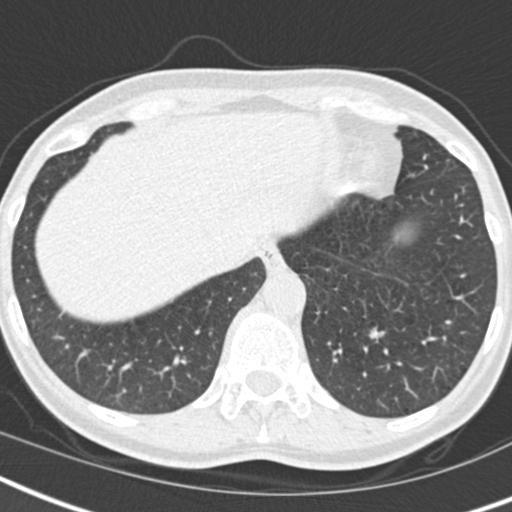
Low-dose screening chest CT, one axial slice. Position 44 of 173 along the scan axis. Reconstruction kernel B30f. 120 kVp. Lung window (W 1500 / L -600 HU). 2 mm slice thickness. 512 × 512 image matrix, field of view 293 × 293 mm.
Annotated regions visible in this slice (expert manual segmentation):
- lesion 1 (tumor, lower lobe of left lung): bounding box [x1, y1, x2, y2] px = [368, 327, 385, 342]